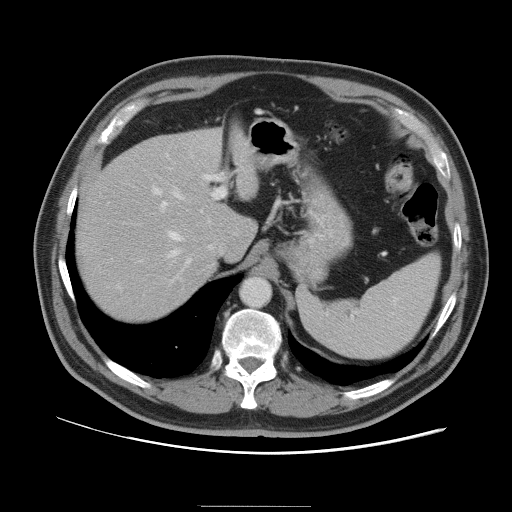
Contrast-enhanced abdominal CT, one axial slice; slice 73 of 105 in the series (ordered by position); 120 kVp; intravenous contrast given; soft-tissue window (W 400 / L 40 HU); 512 × 512 image matrix, field of view 399 × 399 mm. Male patient, age 64 years. From the clinical record (not read from this slice): diagnosis: colorectal cancer liver metastases, imaged before liver resection; multiple liver metastases: yes; largest metastasis: 3 cm; chemotherapy before resection: yes.
Annotated regions visible in this slice (manually delineated by an expert):
- hepatic veins: box from (x=169, y=191) to (x=185, y=257) px
- liver: (x=76, y=129)–(x=256, y=322)
- planned liver remnant (the part of the liver to remain after resection): (x=76, y=144)–(x=254, y=321)
- portal vein (with intrahepatic branches): (x=152, y=174)–(x=226, y=265)